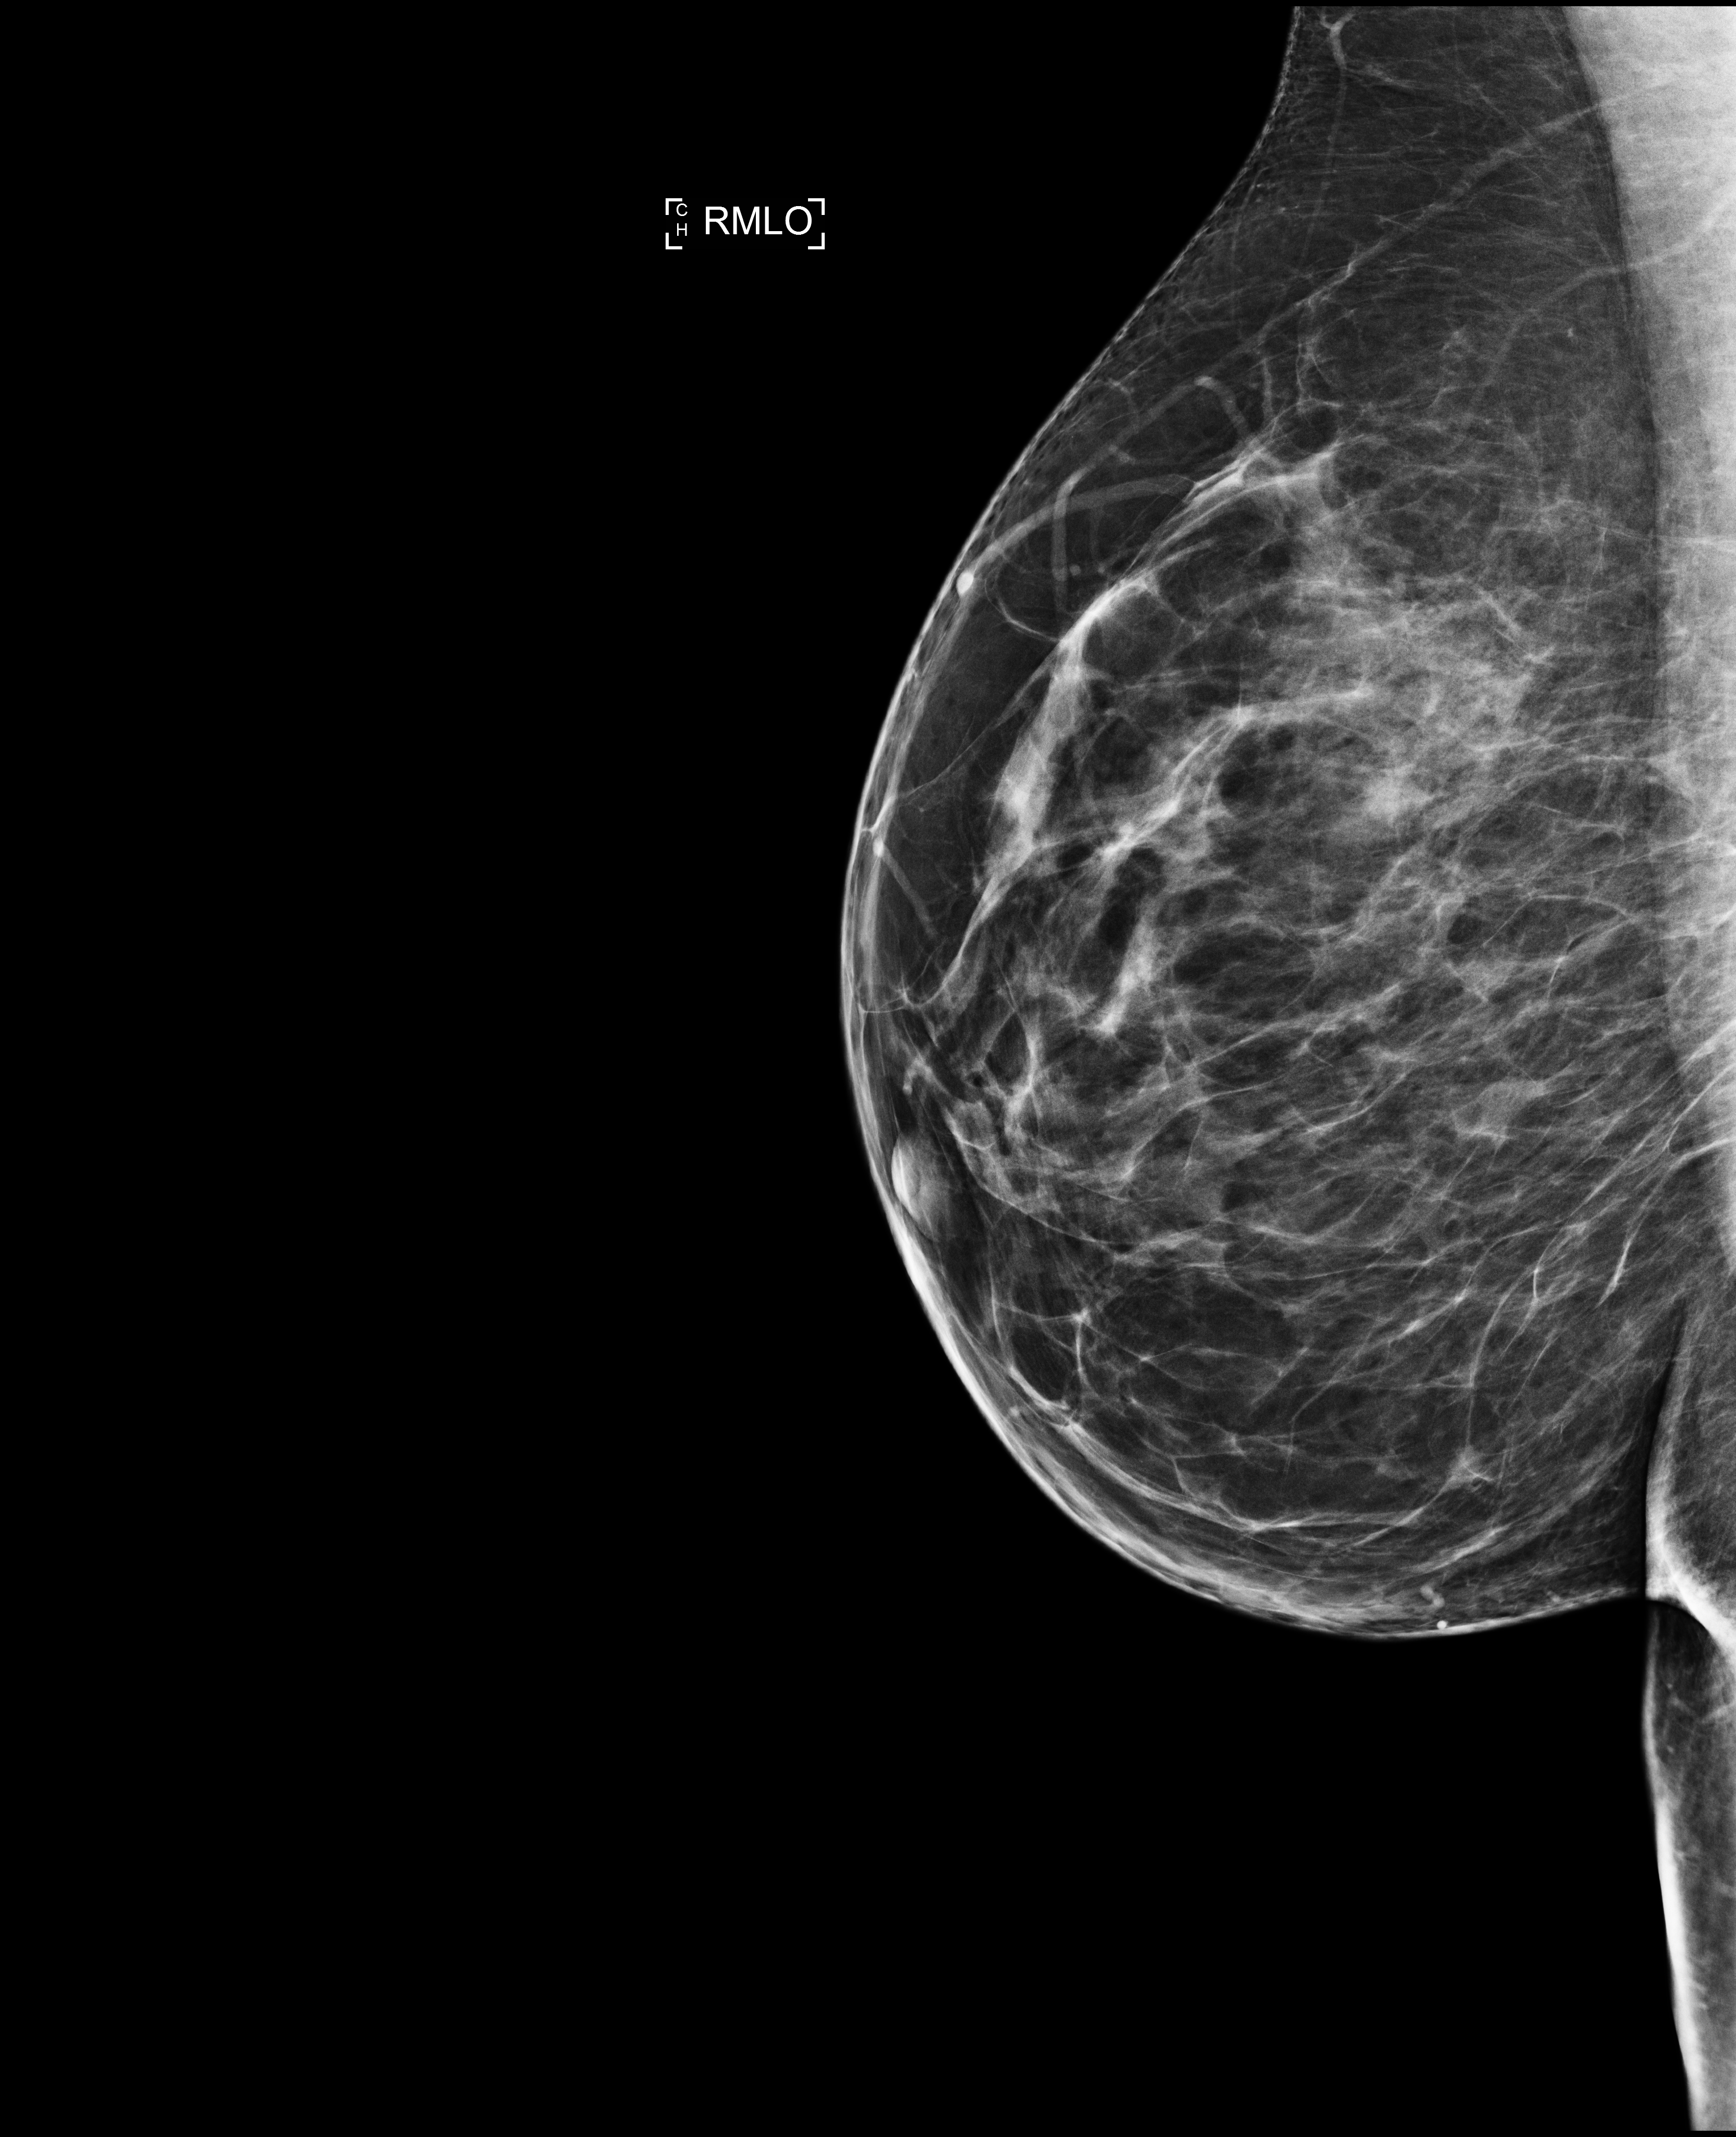
Full-field digital mammogram (FFDM), right breast, mediolateral oblique (MLO) view, annual screening mammography examination. Female patient, age 40 years.
- BI-RADS breast density category at the screening exam (both breasts, scale 1–4): 2
- final BI-RADS category for the screening round (tomosynthesis exam, both breasts): category 1
- recall: no recall after this screen